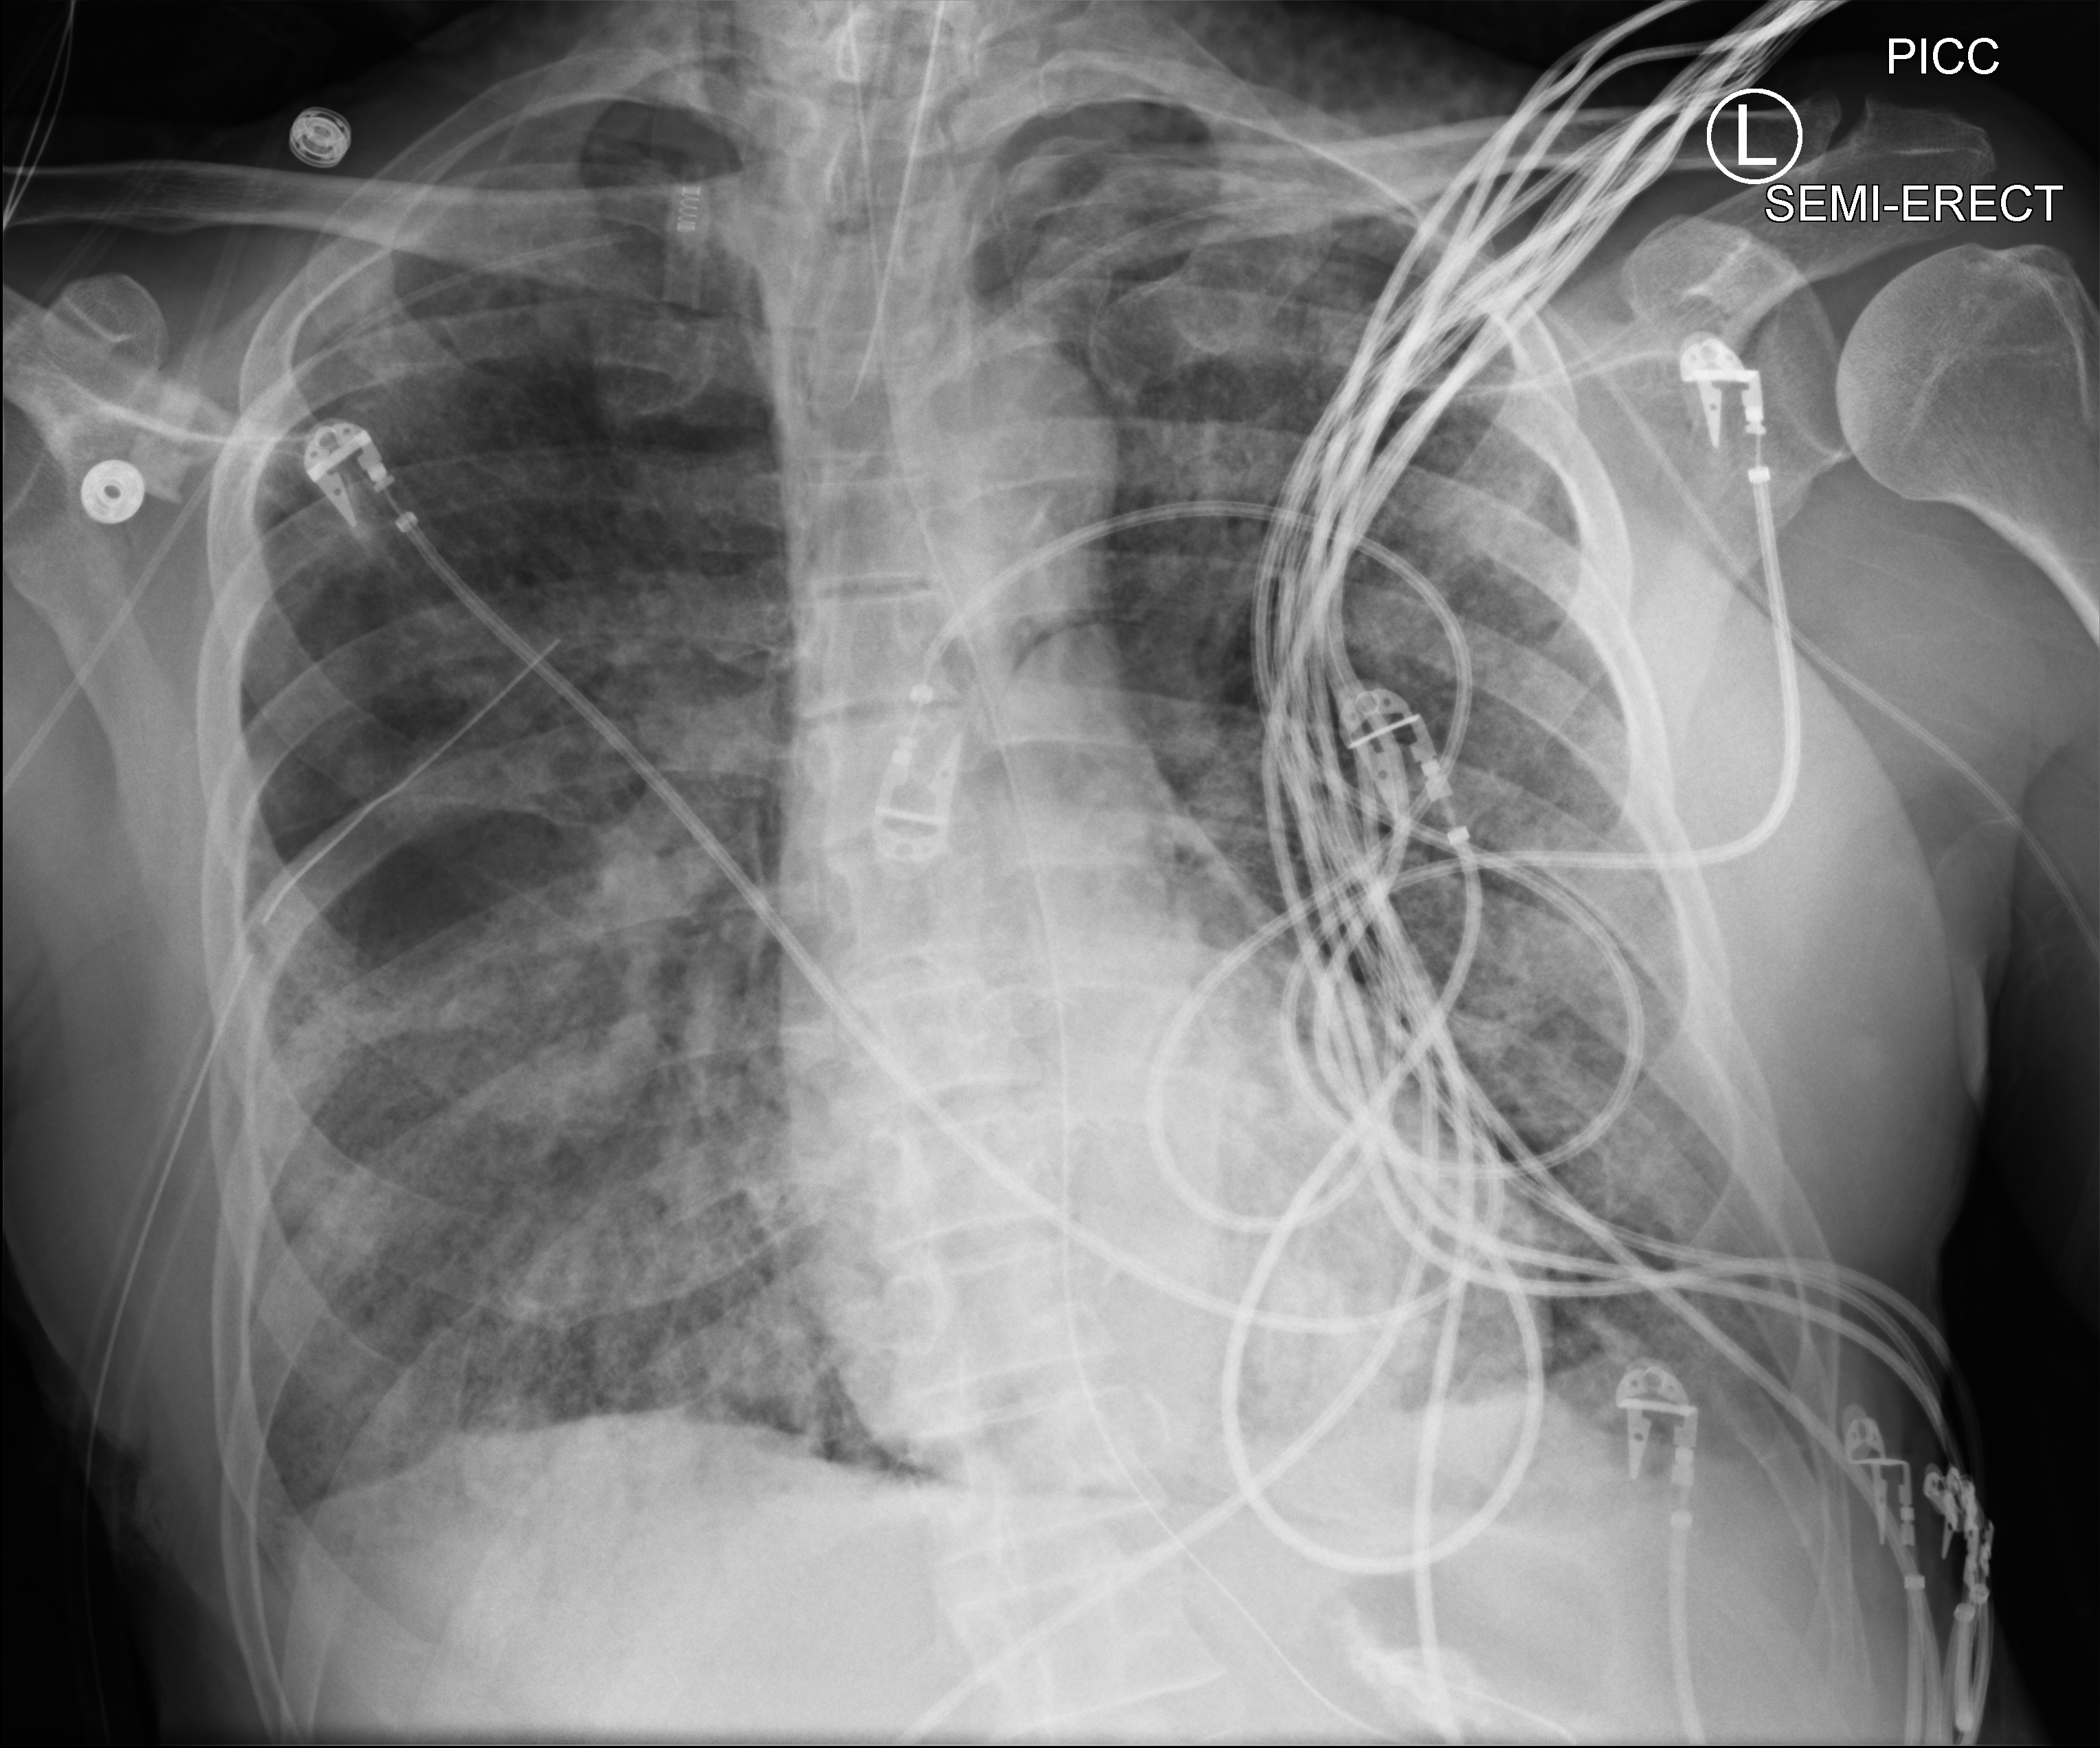
Portable chest radiograph; anteroposterior (AP) projection. Male patient hospitalised with COVID-19, age 60–74 years.
Hospital-stay facts (about this admission, not read from this image; timing relative to this image not recorded):
- mechanically ventilated during this hospital stay: yes